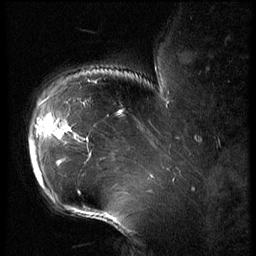
Breast MRI (dynamic contrast-enhanced), one sagittal slice; position 49 of 62 along the scan axis; 3 images stored at this slice position (order not interpretable as contrast timing); 1.5 T; TE 4.2 ms, TR 9 ms; 2.5 mm slice thickness; 256 × 256 image matrix, field of view 180 × 180 mm. Female patient, age 43 years. From the clinical record (not read from this slice): setting: breast cancer imaged before/during neoadjuvant chemotherapy; receptor status: HER2-positive.
Structures marked on this image (semi-automatically segmented with operator editing):
- analysis volume of interest (the breast-tissue region the enhancement analysis was run in; not a lesion): bounding box (x1, y1, x2, y2) in pixels: (27, 90, 82, 203)
- tumour enhancement mask (voxels above the 140 % enhancement threshold inside the analysis volume of interest): (30, 114, 79, 185)